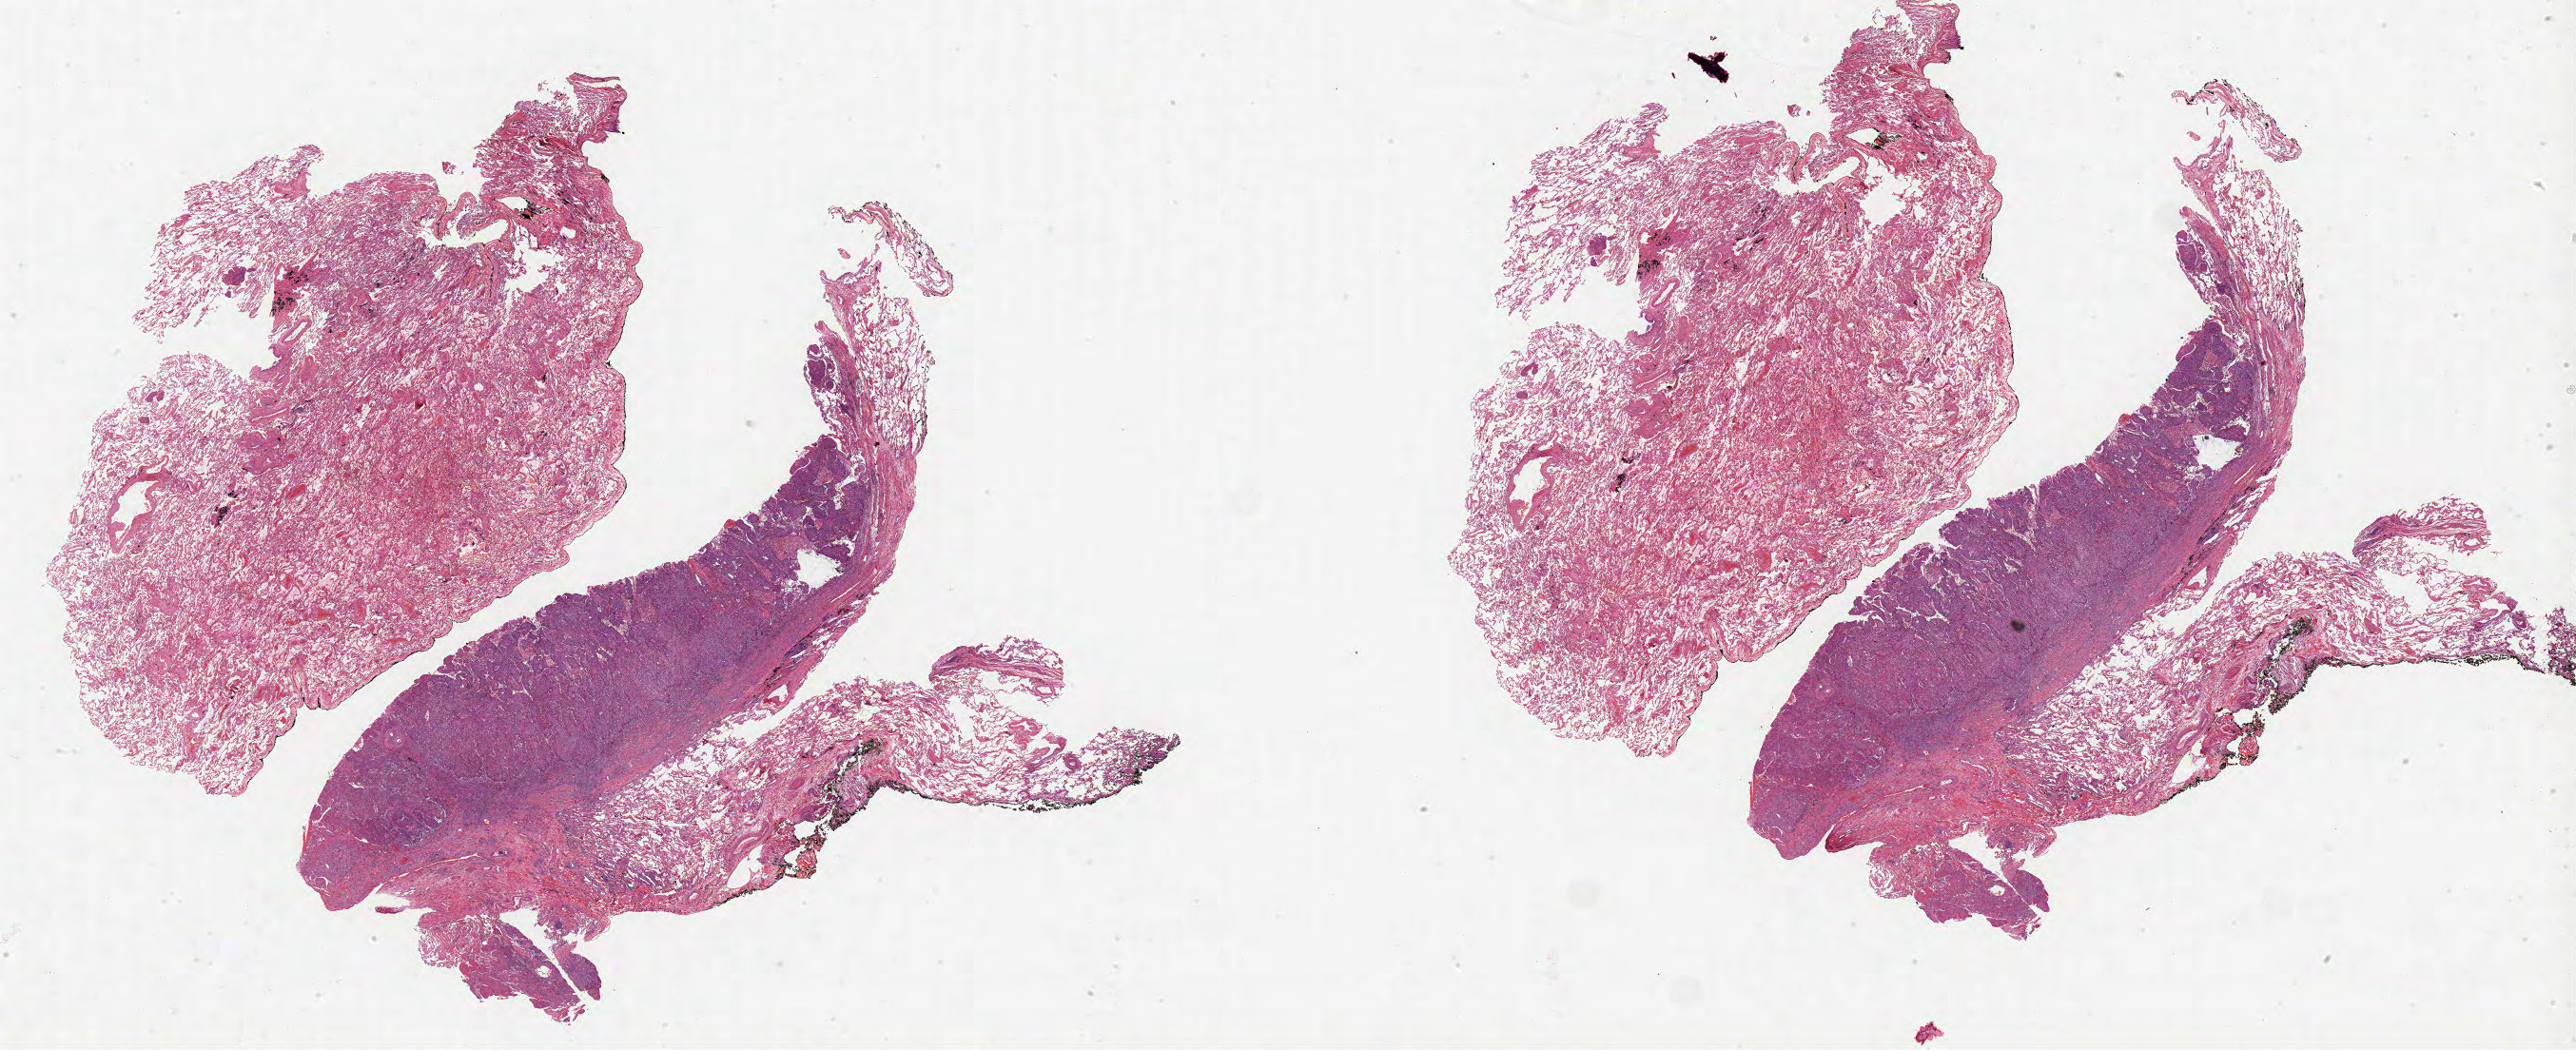
Digitized H&E-stained tissue section (whole slide) — low-resolution overview of the scanned area, about 43.7 x 17.8 mm (acquisition: 20x scan); formalin-fixed paraffin-embedded (FFPE) diagnostic section; primary tumour sample from the lung. Patient: male, age at initial diagnosis 73 years.
AJCC pathologic stage: IB (7th edition). Diagnosis: Squamous cell carcinoma, NOS. TNM: T2a N0 M0.